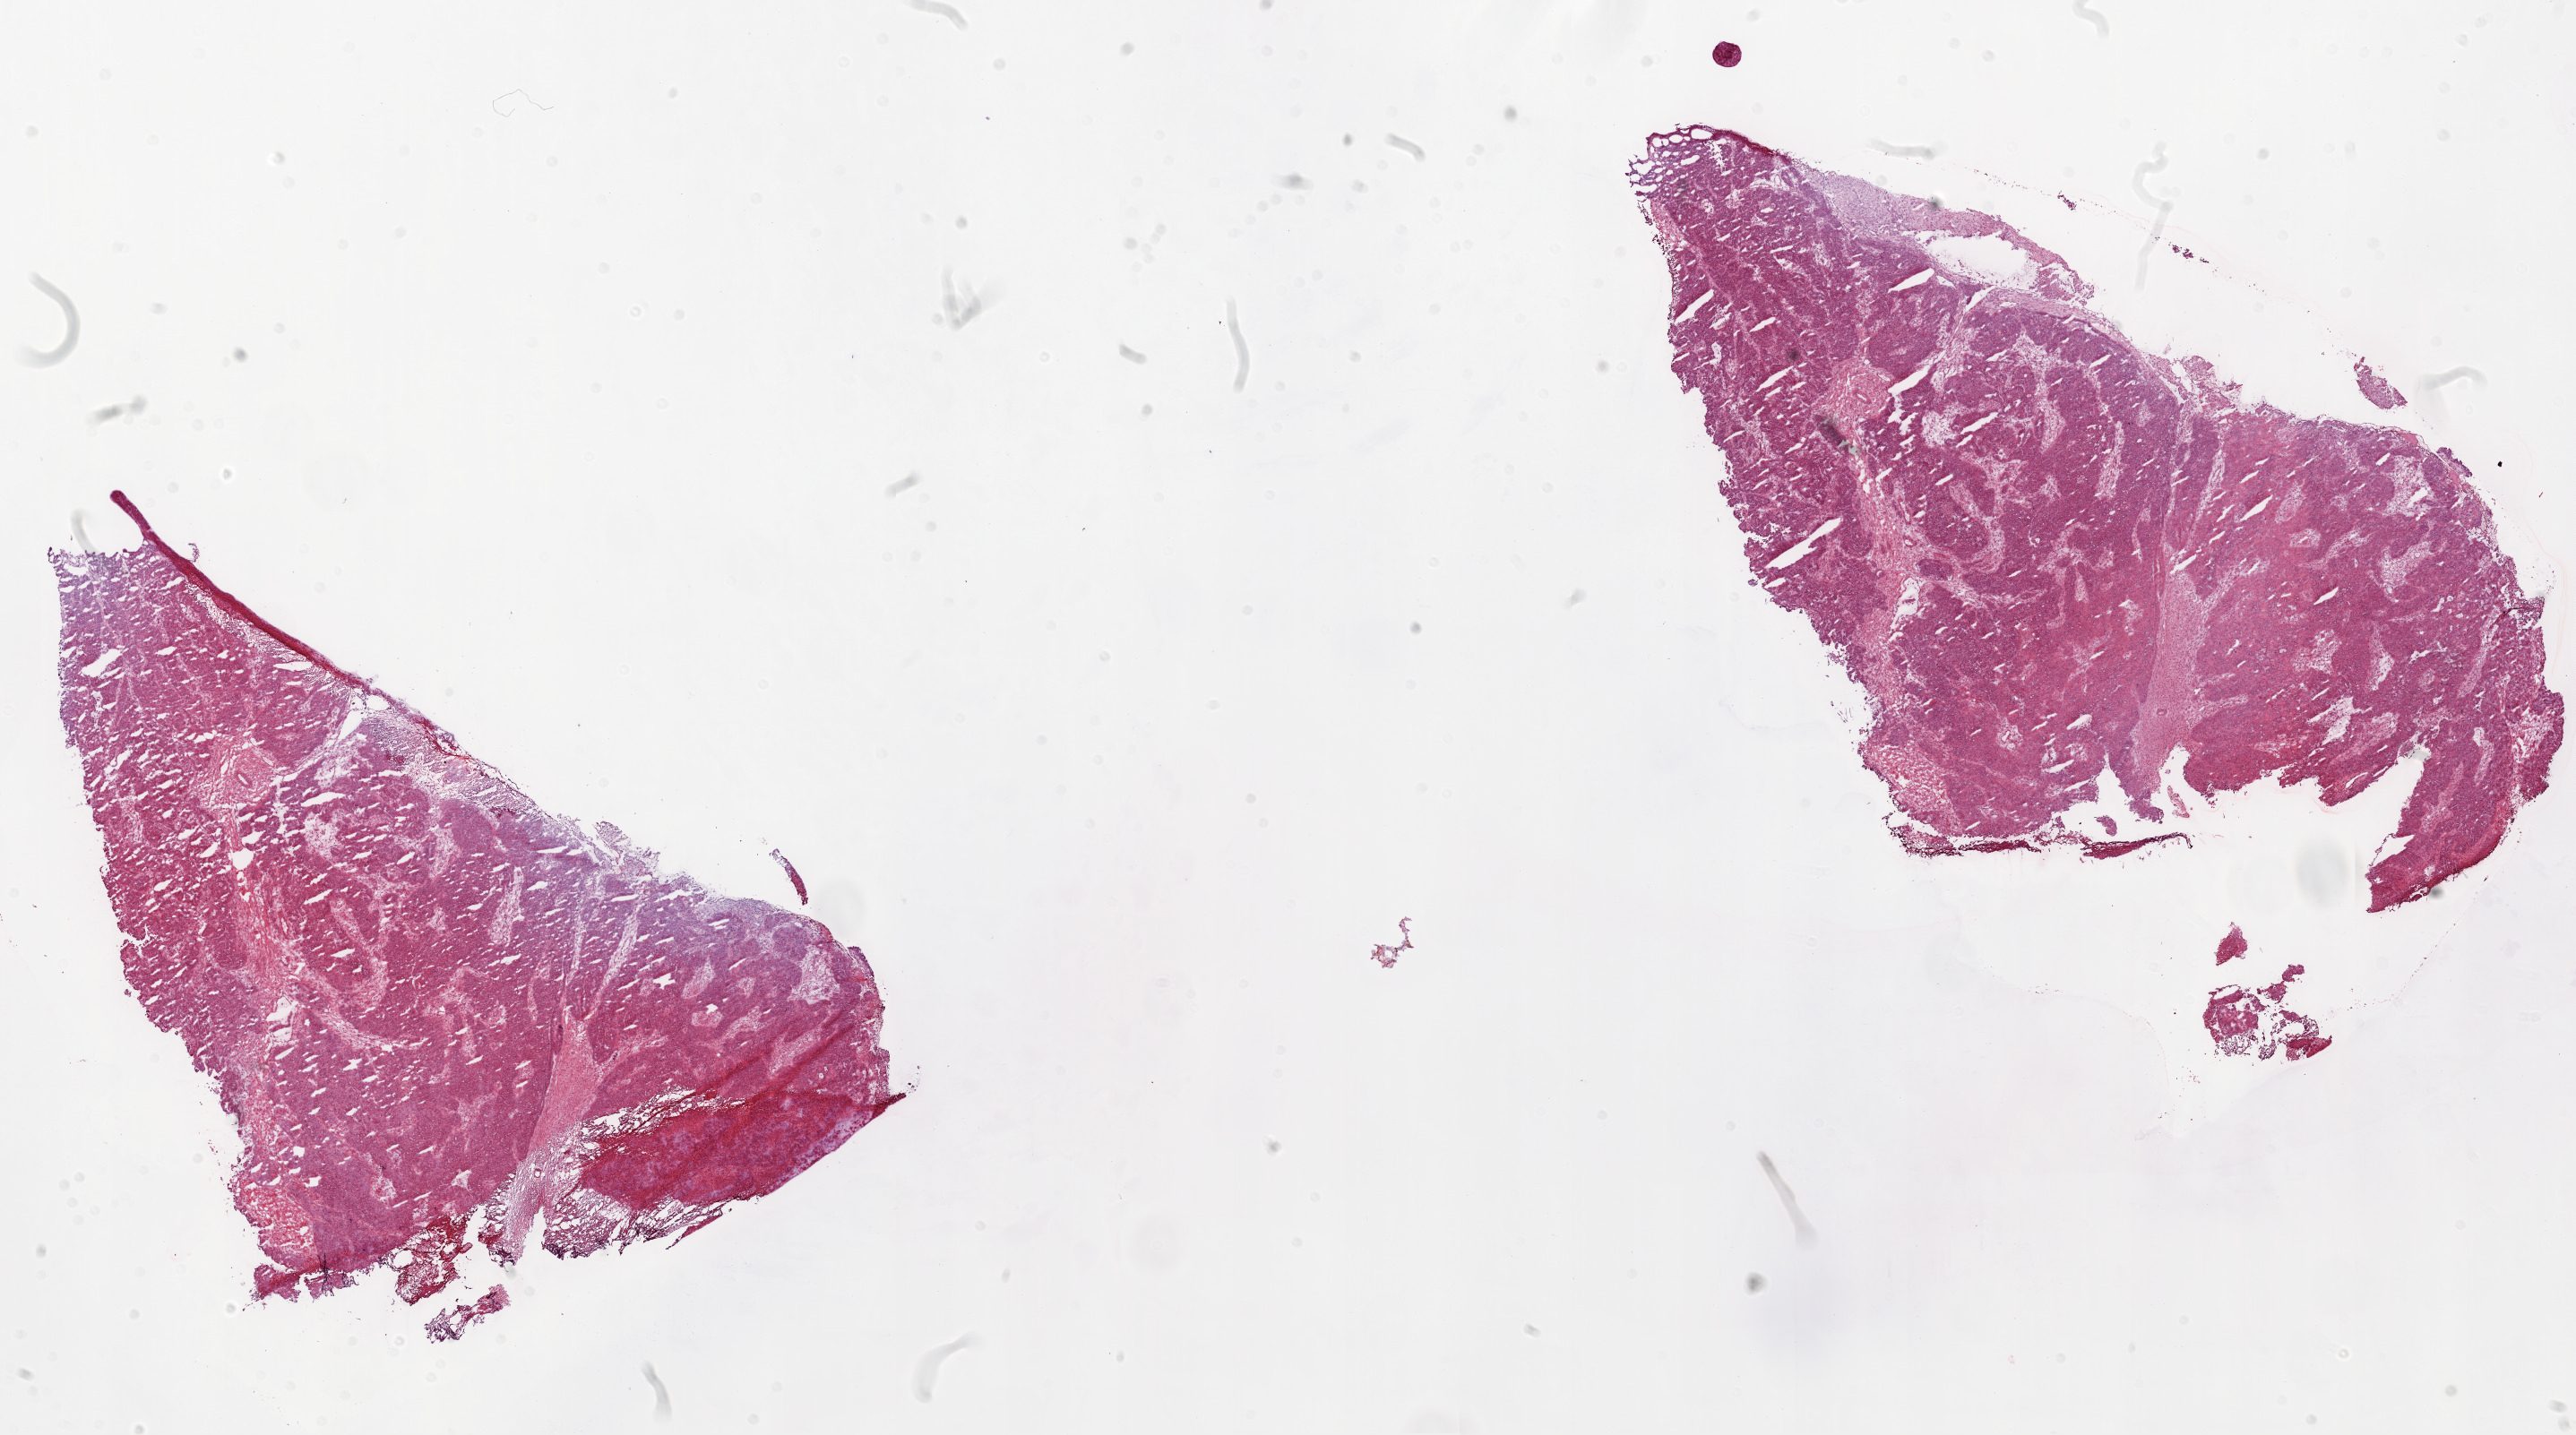
H&E whole-slide image — low-resolution overview of the scanned area, about 23.1 x 12.9 mm. Frozen section from the top of the tissue portion. Primary tumour sample from the ovary. Patient: female, age at initial diagnosis 30 years. Histologic grade: G3 (poorly differentiated). Slide review estimates, as recorded: tumour cells 85%, tumour nuclei 85%, normal cells 0%, stromal cells 13%, necrosis 2%.
Laterality: bilateral. FIGO stage: IIIC. Pathologic diagnosis: Serous cystadenocarcinoma, NOS.